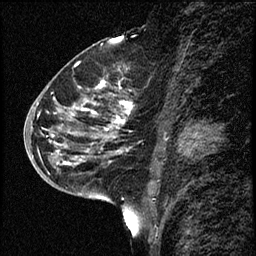
Breast MRI (dynamic contrast-enhanced), one sagittal slice. Slice 33 of 68 in the series (ordered by position). Dynamic contrast-enhanced study with each time point stored as its own series, time point 2 of 3 at this slice position (early post-contrast, ordered by acquisition time). 1.5 T. TE 4.2 ms, TR 17.6 ms. 2 mm slice thickness. 256 × 256 image matrix. Patient: female, 52 years. From the clinical record (not read from this slice): setting: breast cancer imaged before/during neoadjuvant chemotherapy; receptor status: HER2-positive.
Annotated regions visible in this slice (semi-automatic segmentation, software-assisted and operator-edited):
- analysis volume of interest (the breast-tissue region the enhancement analysis was run in; not a lesion): bounding box [x1, y1, x2, y2] px = [50, 61, 140, 184]
- tumour enhancement mask (voxels above the 100 % enhancement threshold inside the analysis volume of interest): [53, 81, 130, 165]